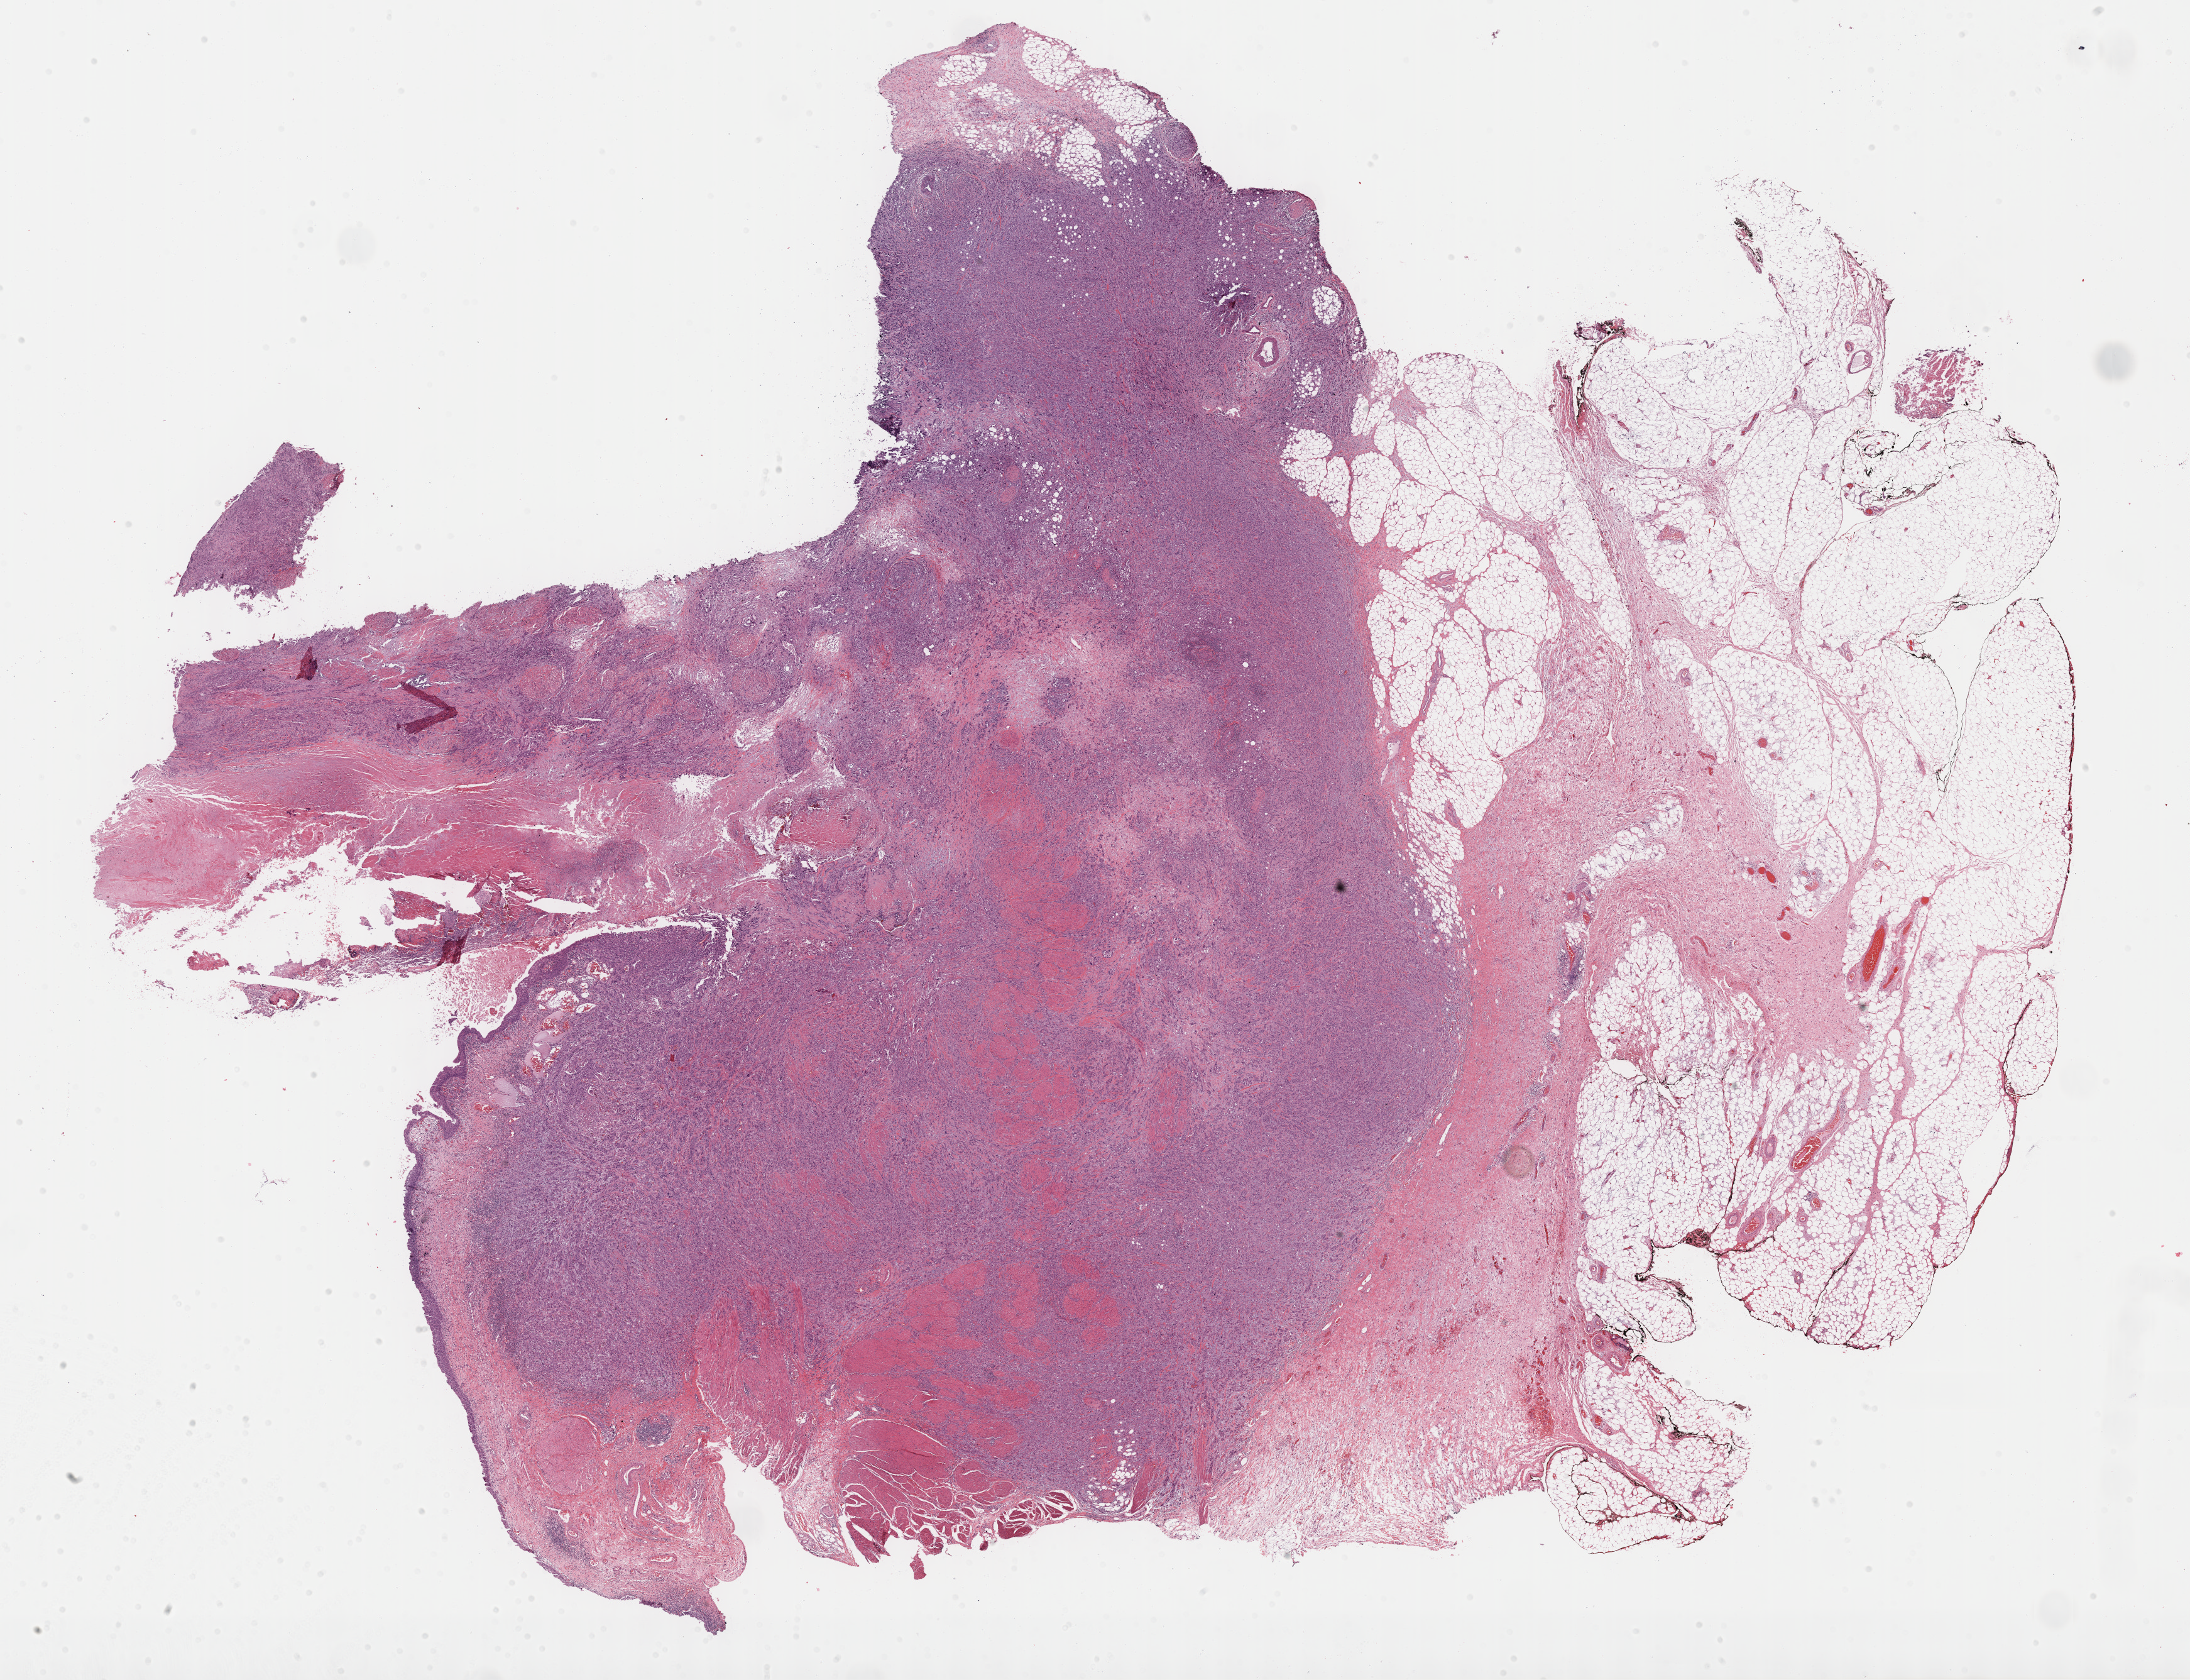
Digitized H&E tissue section (whole slide) — a low-resolution overview of the entire scanned area, about 28.2 x 21.6 mm; formalin-fixed paraffin-embedded (FFPE) diagnostic section; primary tumour sample from the bladder. Patient: female, age at initial diagnosis 69 years. Histologic grade: high grade.
* AJCC pathologic stage: IV (4th edition)
* histologic diagnosis: Transitional cell carcinoma
* lymph nodes positive (case pathology): 2 of 52 examined